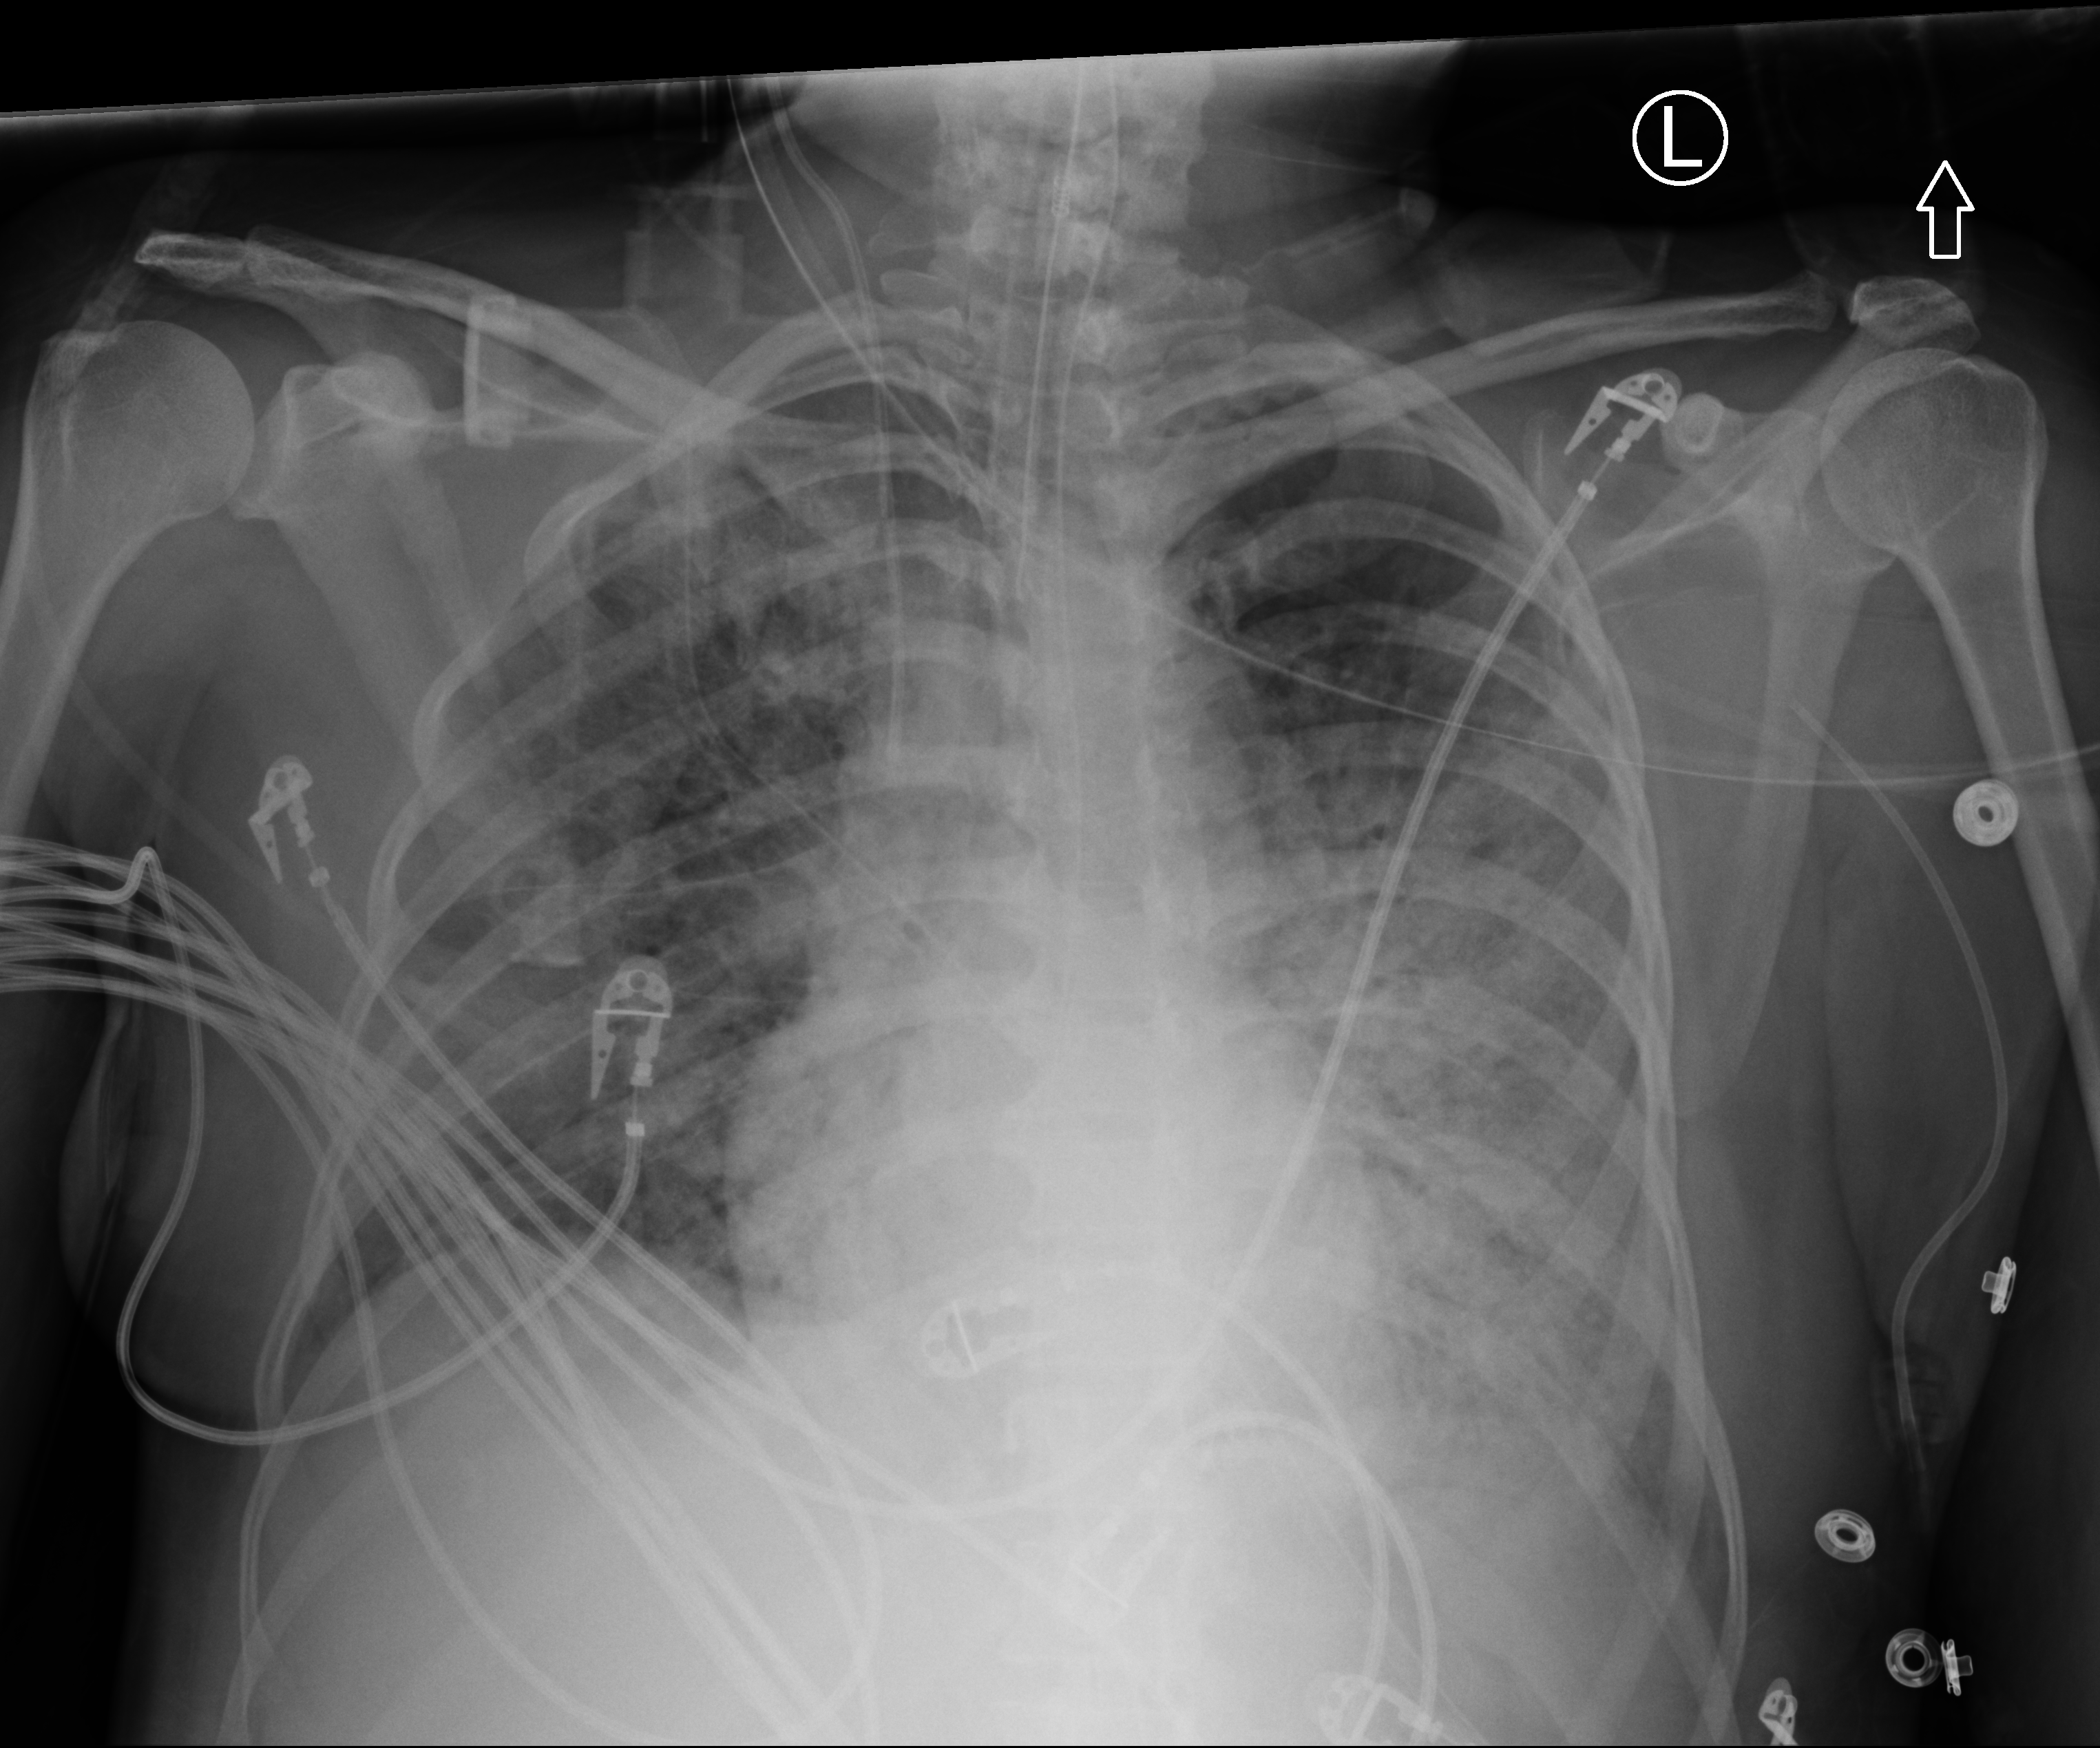
Portable chest radiograph; anteroposterior (AP) projection. Patient hospitalised with COVID-19; female, aged 18–59 years.
Hospital-stay facts (about this admission, not read from this image; timing relative to this image not recorded):
- mechanically ventilated during this hospital stay: yes
- length of hospital stay: 71 days
- other chronic lung disease (admission record): no